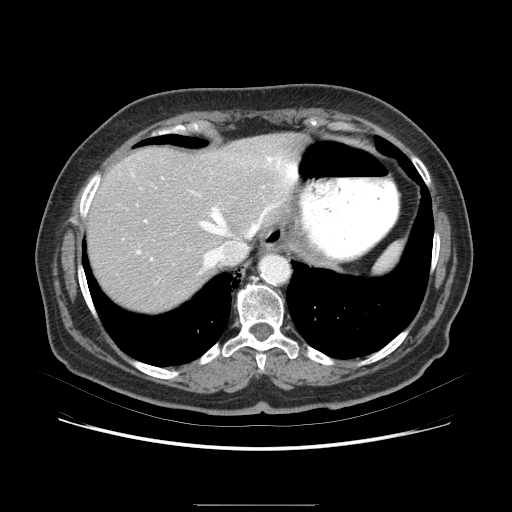
Contrast-enhanced abdominal CT (liver protocol), one axial slice; slice 65 of 79 in the series (ordered by position); 120 kVp; soft-tissue window (W 400 / L 40 HU); 2.5 mm slice thickness; 512 × 512 image matrix, field of view 380 × 380 mm. From the clinical record (not read from this slice): diagnosis: hepatocellular carcinoma (patient treated with transarterial chemoembolisation; whether this scan precedes or follows treatment is not stated here); TNM stage (as recorded): Stage-I; Child-Pugh class: A; tumour nodularity: uninodular.
Structures marked on this image (semi-automatically segmented with operator editing):
- liver parenchyma outside the tumour (the mass and vessels are separate outlines, so this box may not span the whole liver): bounding box <92,141,320,291> (left, top, right, bottom; pixels)
- liver vessels: <147,220,297,225>